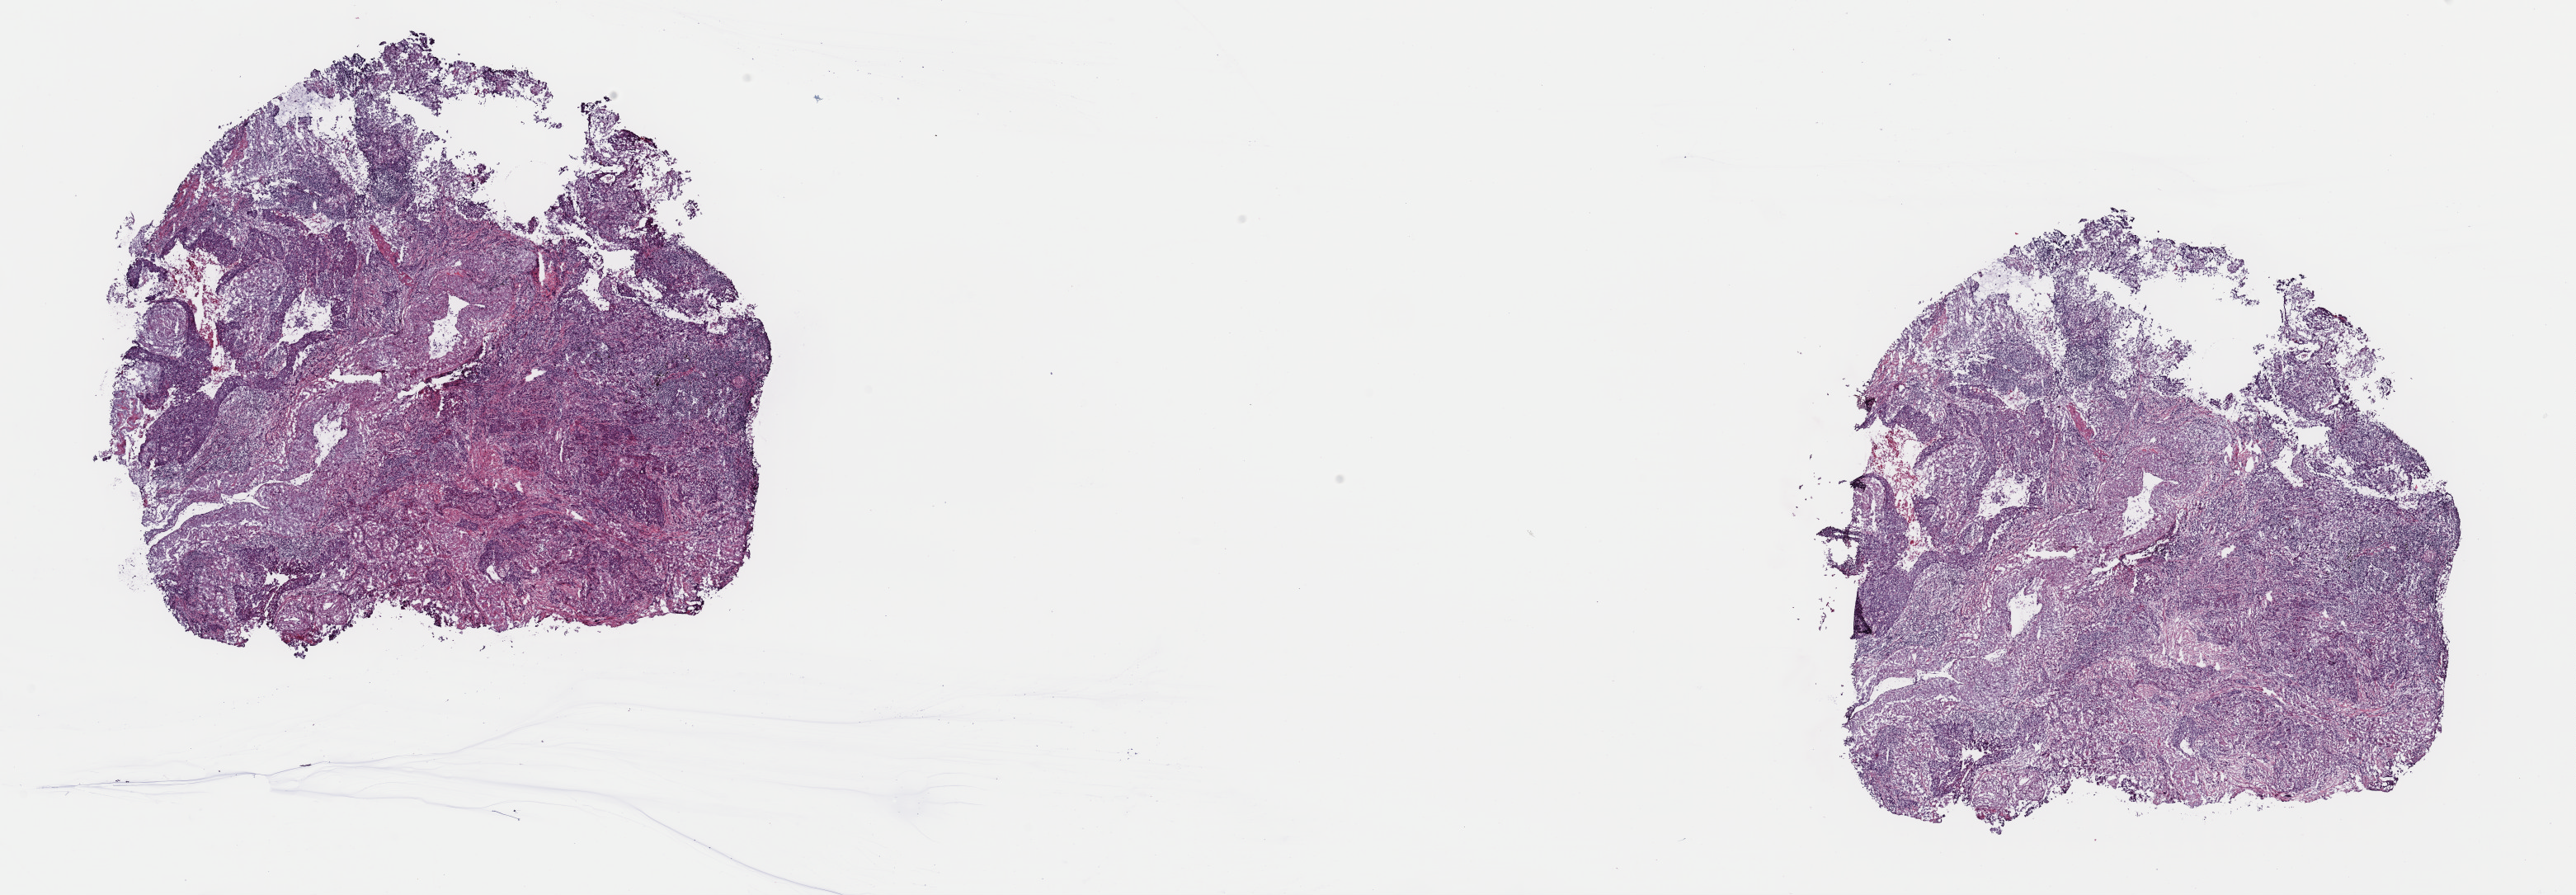
Digitized H&E-stained tissue section (whole slide), shown as a low-resolution overview of the whole scanned area (about 24.7 x 8.6 mm, slide scanned at 40x), frozen section from the top of the tissue portion, primary tumour sample from the lung. Male, age 81 years at initial diagnosis. Composition of this section per pathologist review: tumour cells 97%, tumour nuclei 65%, normal cells 0%, stromal cells 0%, necrosis 3%. Infiltration values recorded for this section: lymphocyte infiltration 5%, monocyte infiltration 1%, neutrophil infiltration 1%.
Diagnosis: Squamous cell carcinoma, NOS (lower lobe, lung). Laterality: left. AJCC pathologic stage: IB.